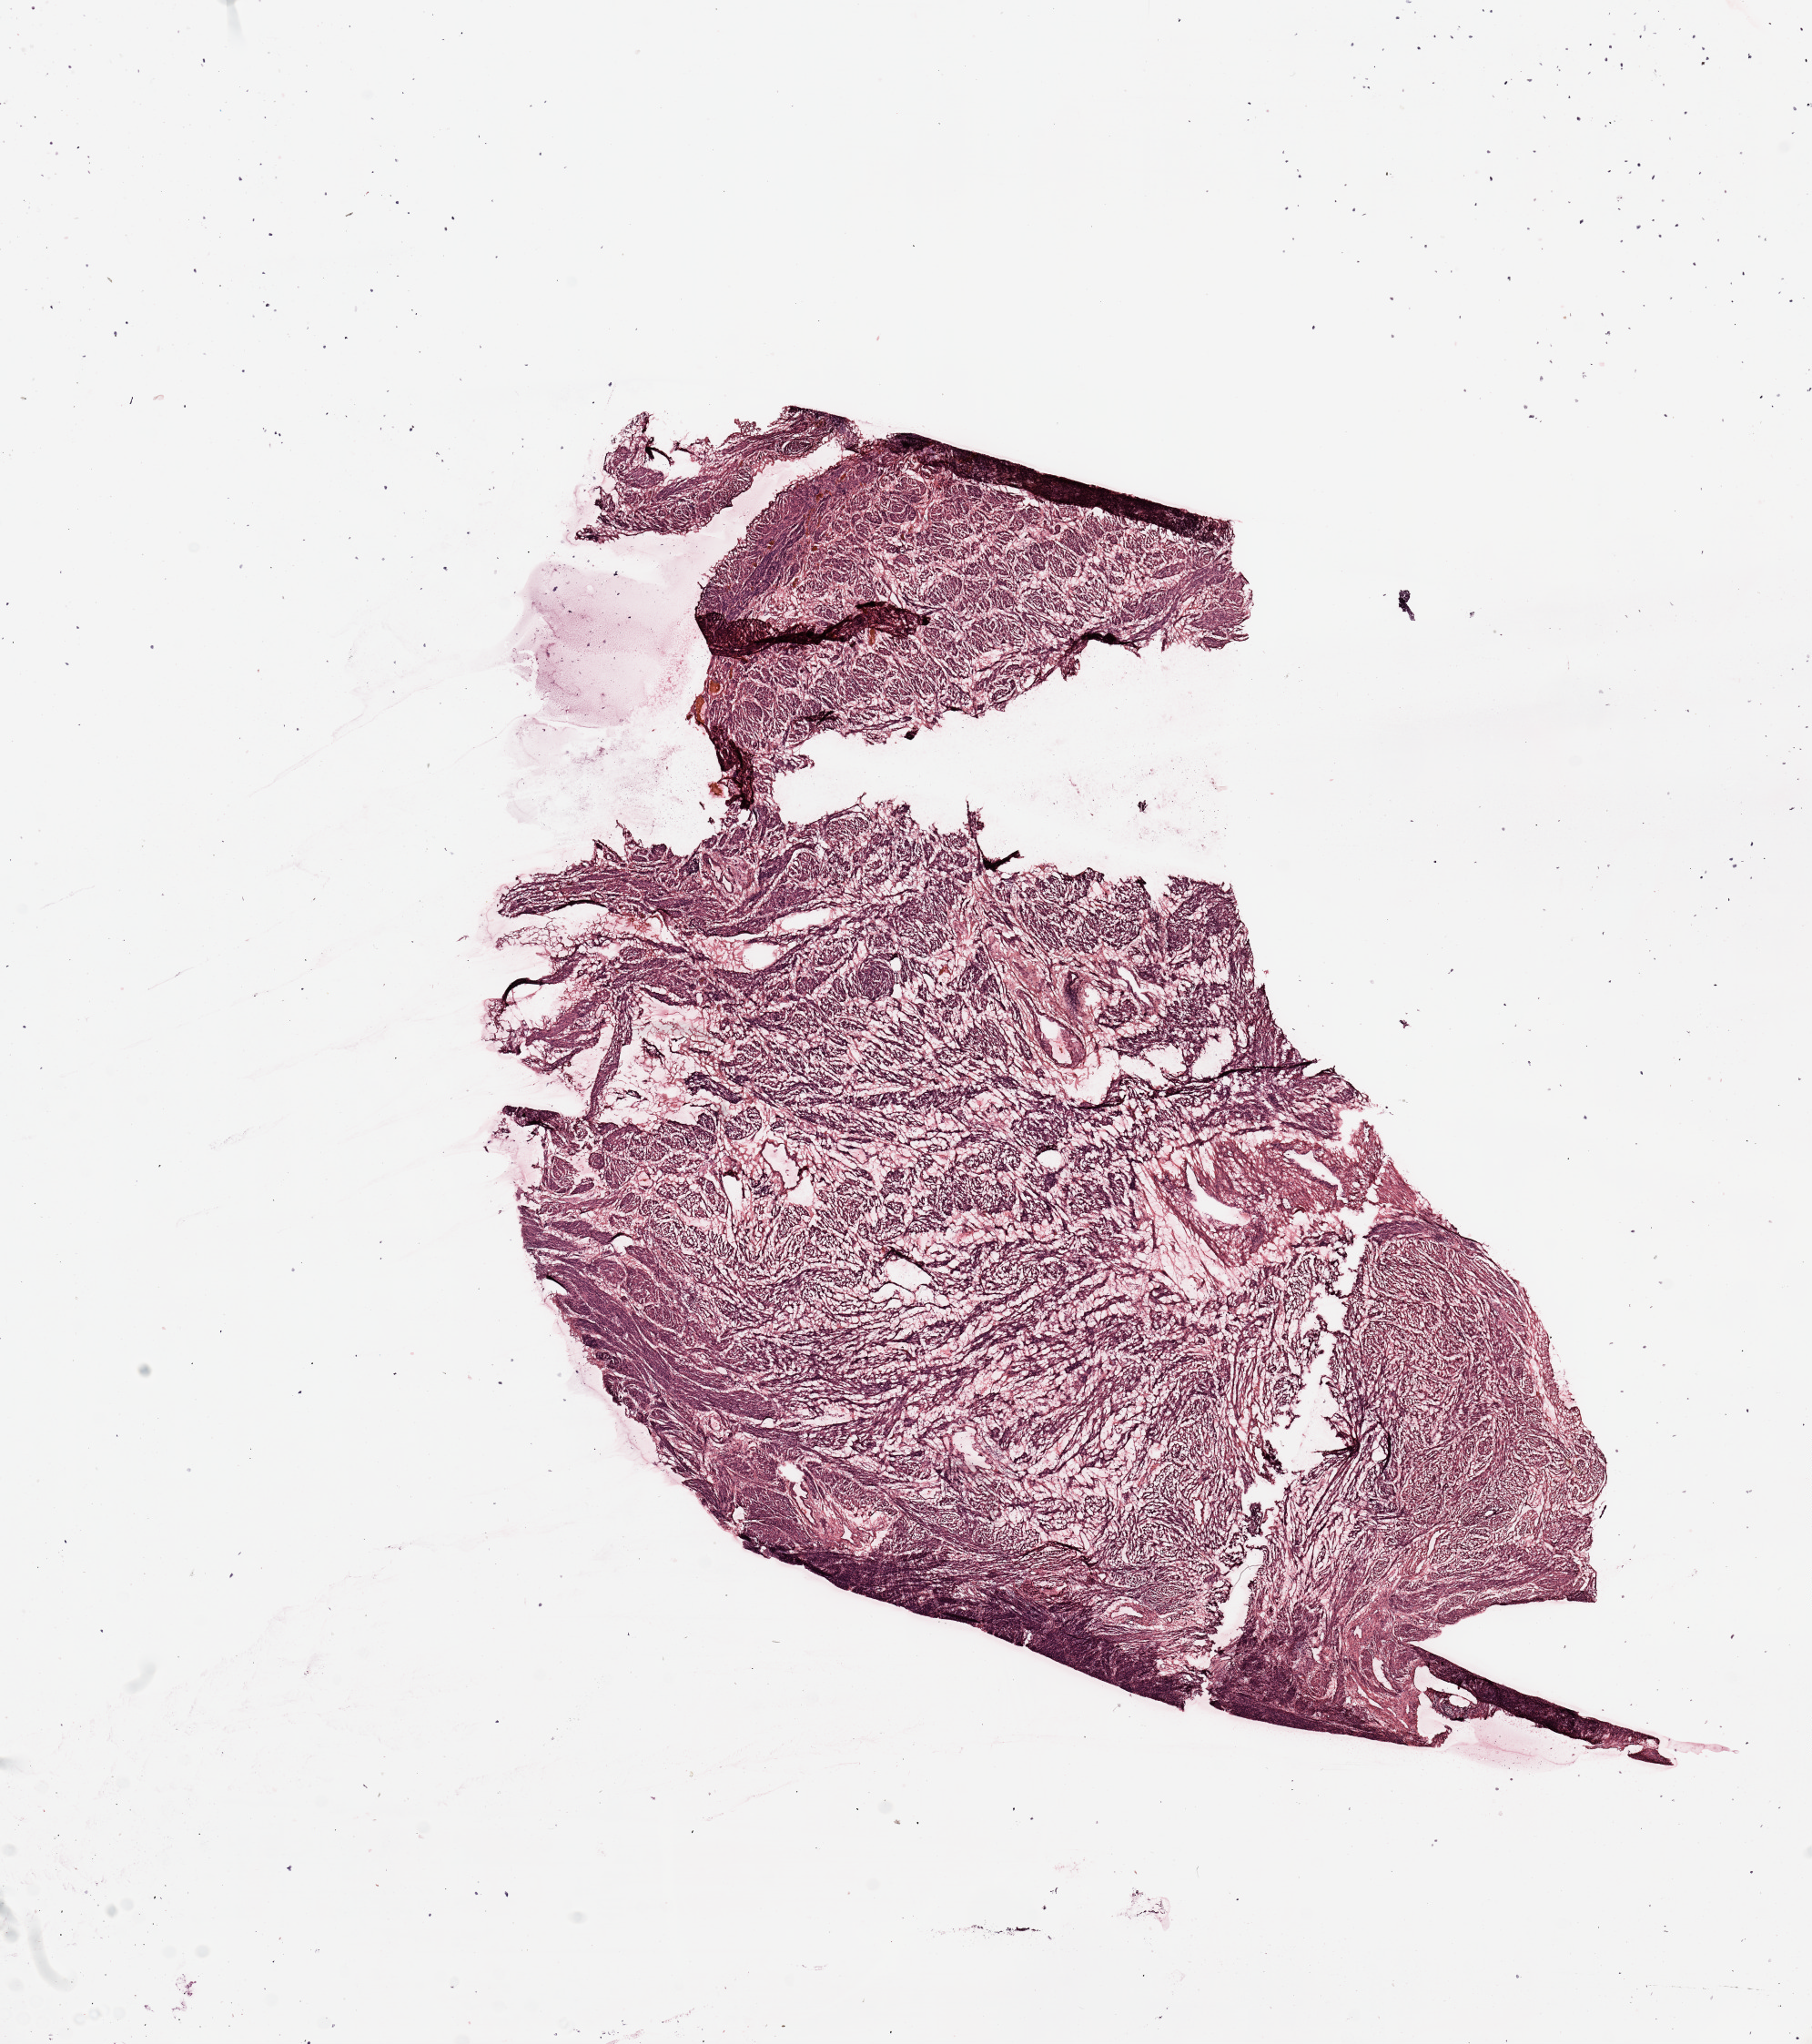
Hematoxylin and eosin (H&E) stained whole-slide image — shown as a low-resolution overview of the whole scanned area (about 15.8 x 17.8 mm). Normal (non-tumour) tissue sample, uterus. 57-year-old female patient.
This section: normal (non-tumour) tissue from the same patient. Patient diagnosis: Endometrioid adenocarcinoma, NOS.